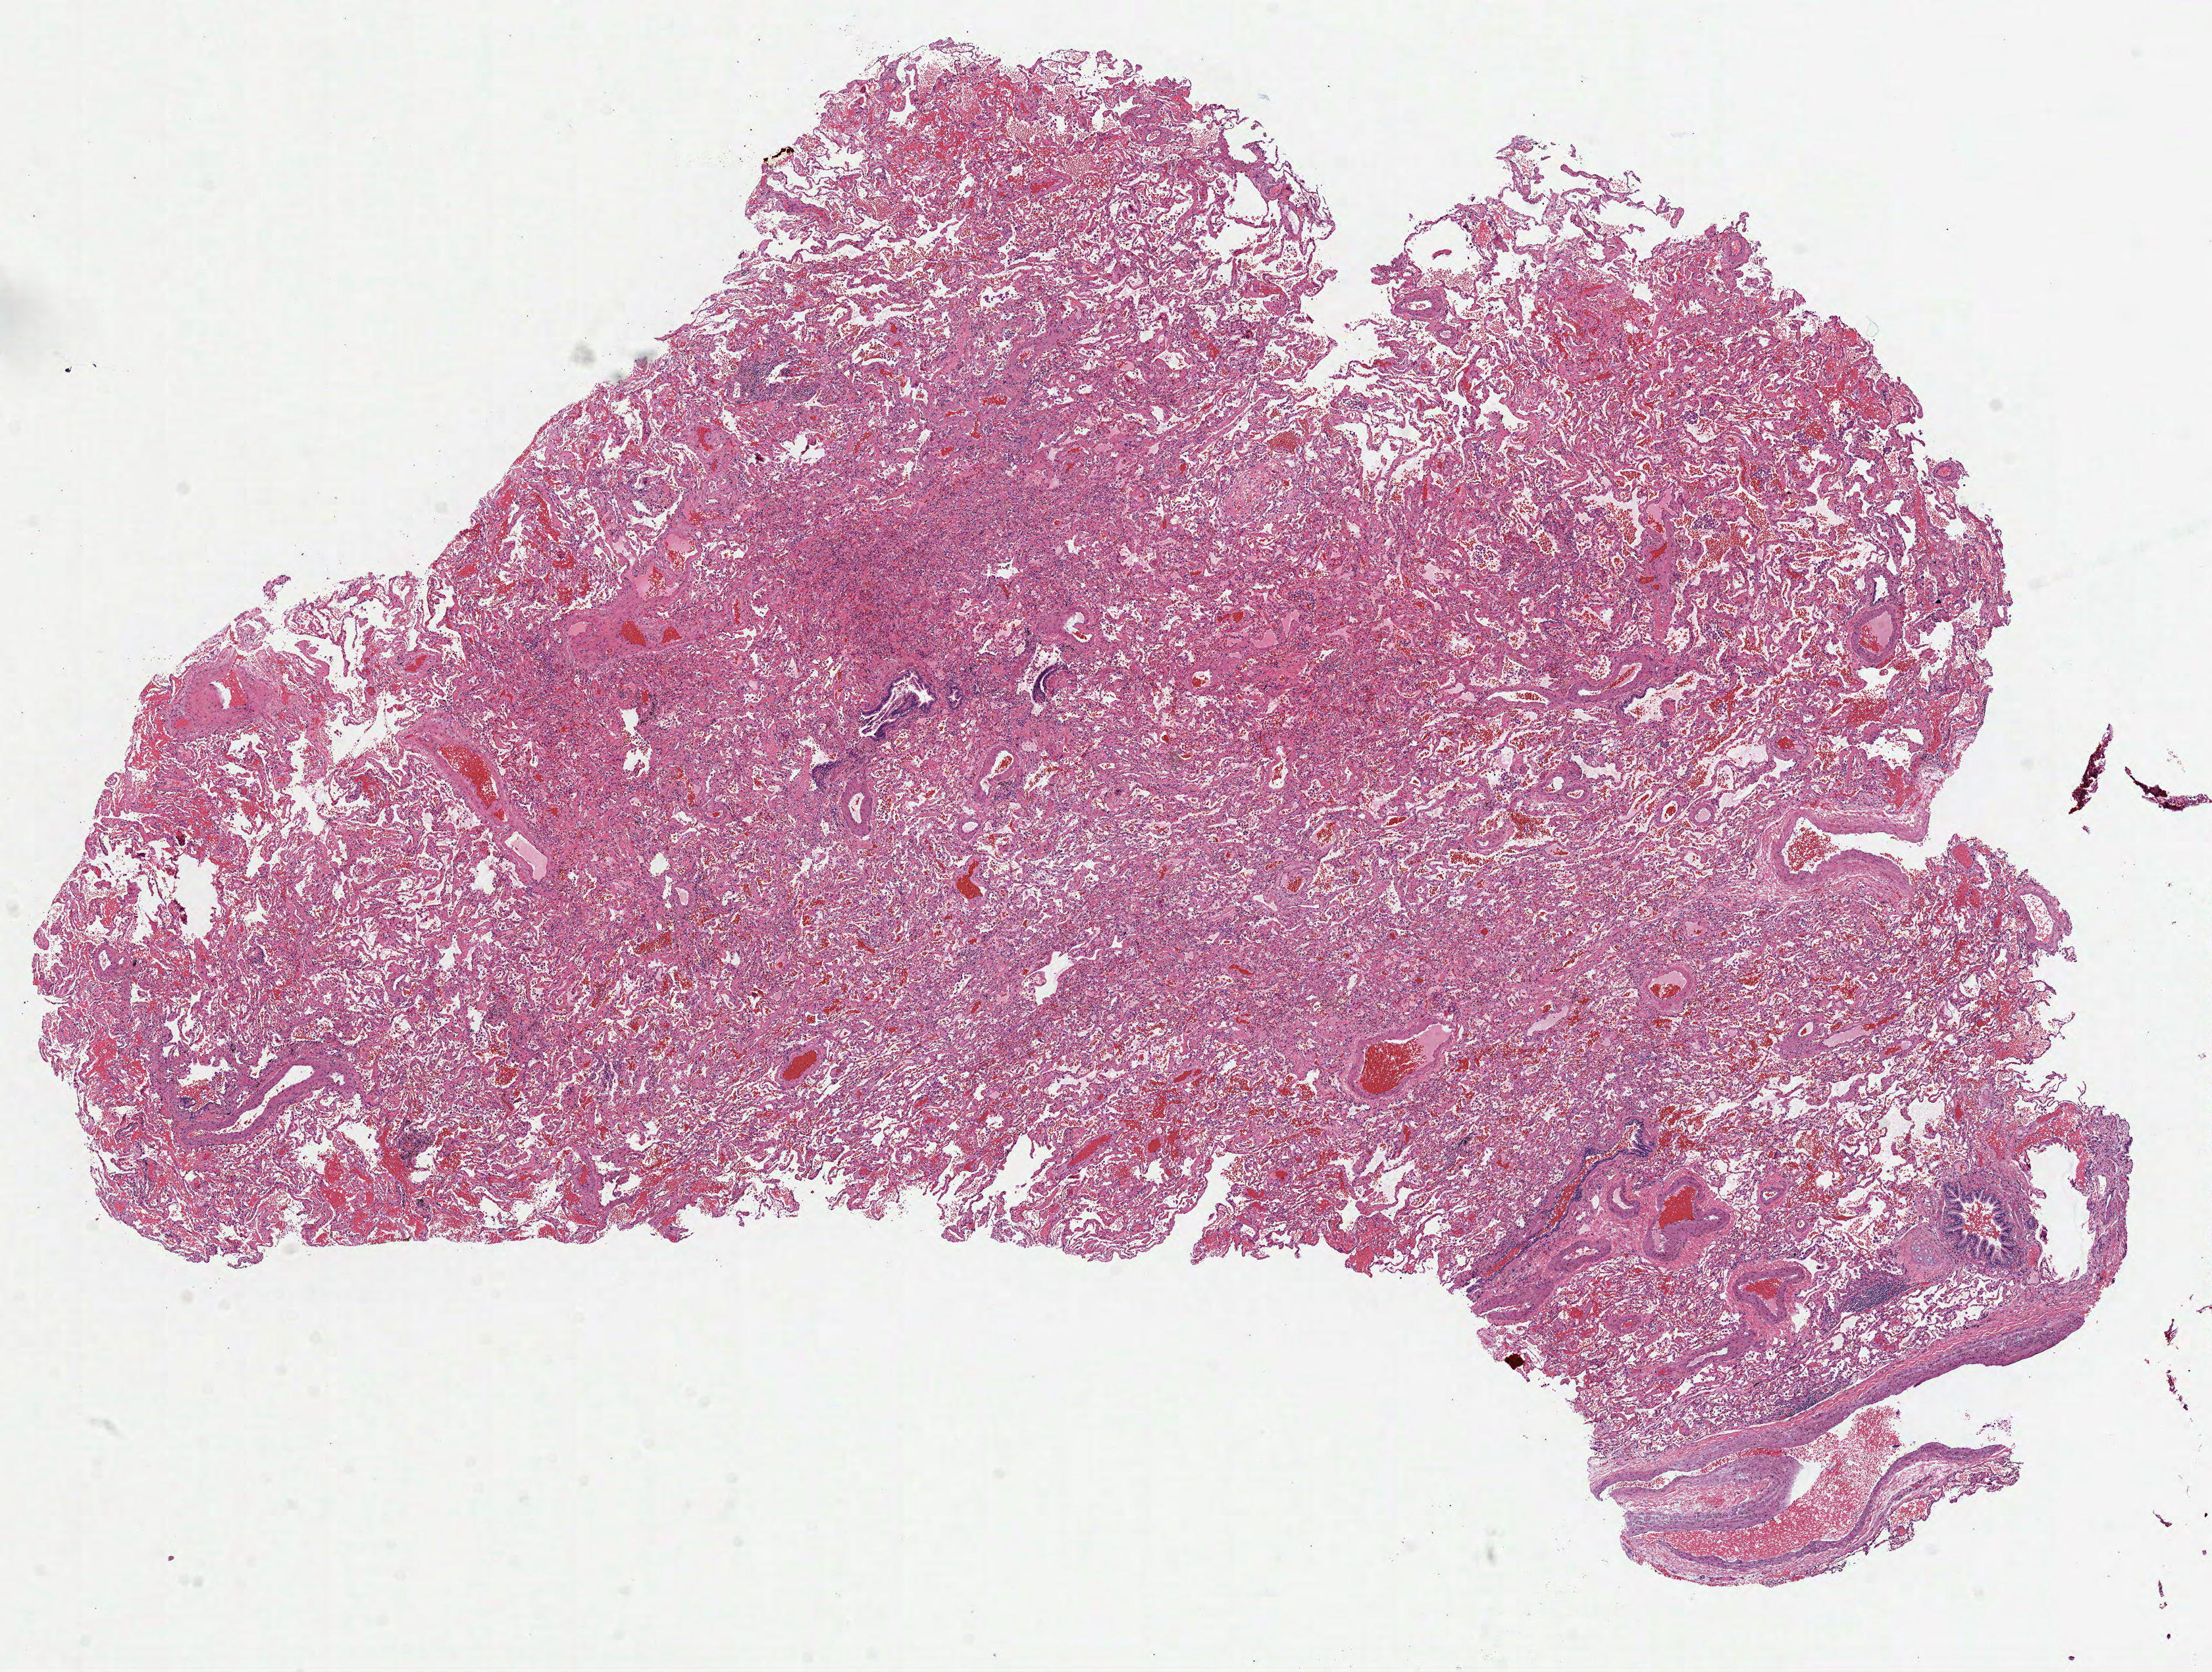
Digitized H&E-stained tissue section (whole slide), a low-resolution overview of the entire scanned area, about 13.6 x 10.2 mm (slide scanned at 40x); frozen section from the top of the tissue portion; solid tissue normal (non-tumour tissue) sample from the lung. Female patient; age at initial diagnosis 62 years.
This section: solid tissue normal sample (biorepository sample class). Patient diagnosis: Adenocarcinoma, NOS (upper lobe, lung).